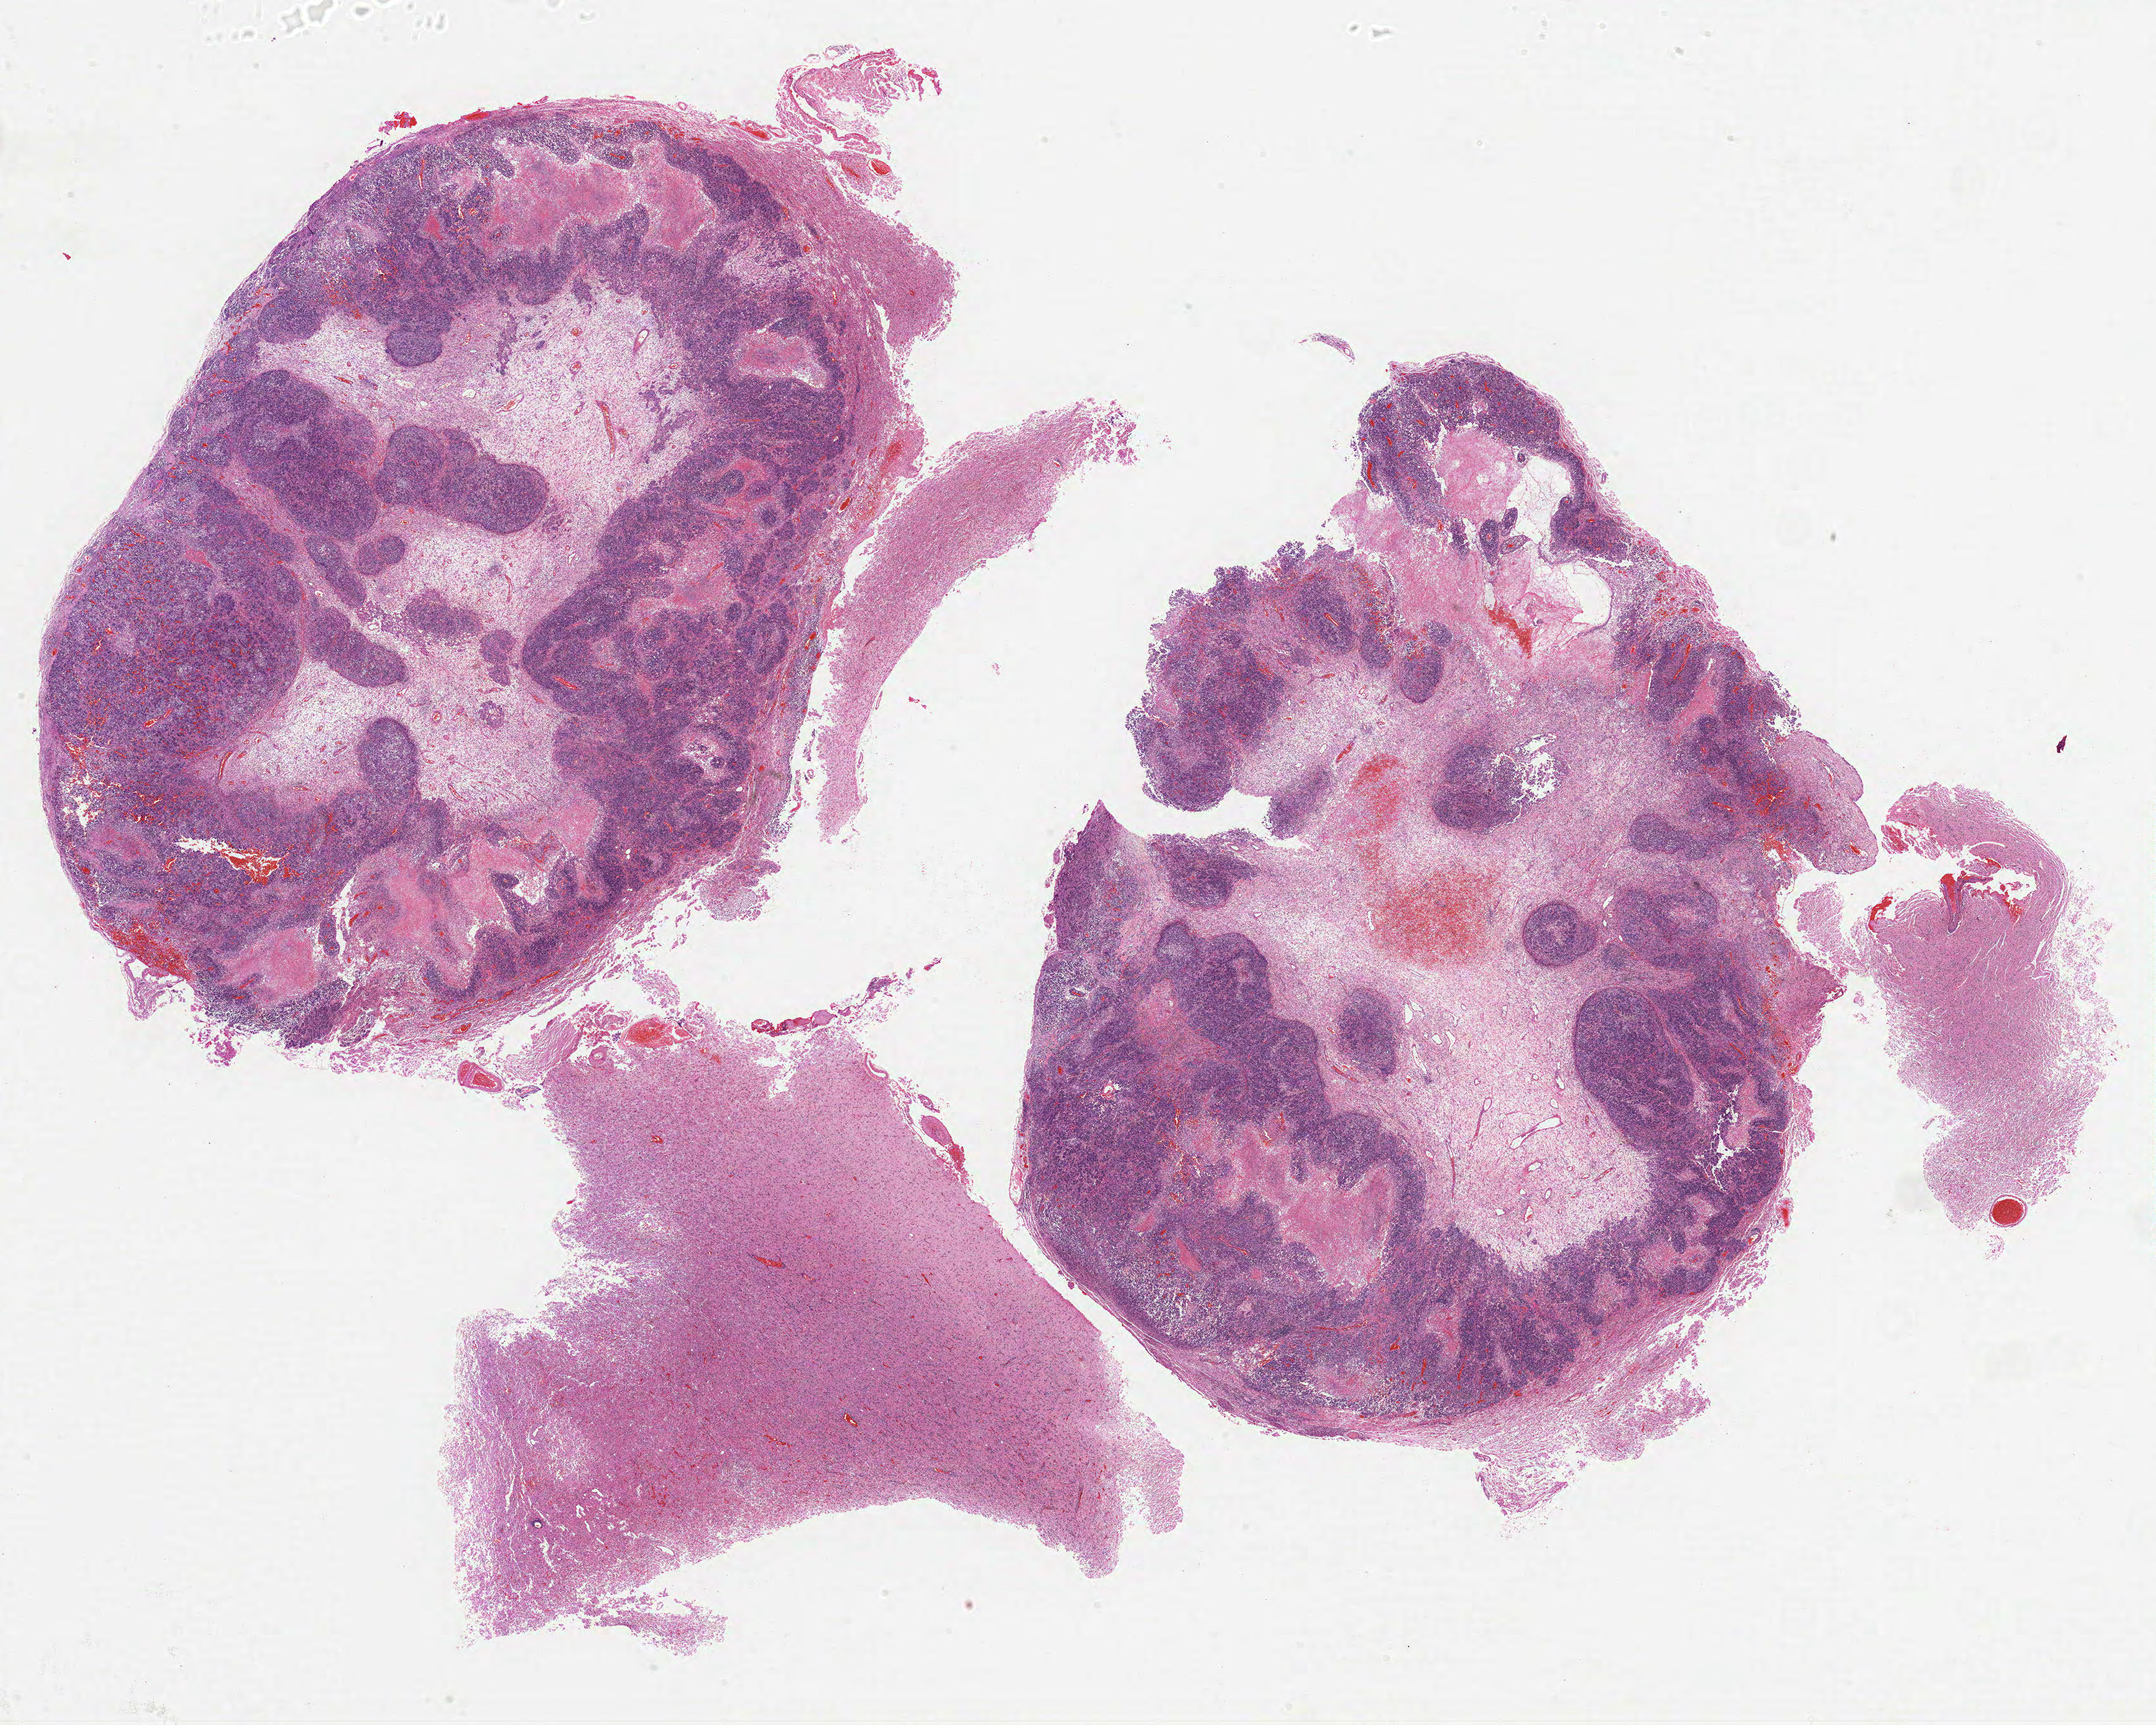
H&E-stained whole-slide image, shown as a low-resolution overview of the whole scanned area (about 27.0 x 21.6 mm), formalin-fixed paraffin-embedded (FFPE) diagnostic section, primary tumour sample from the brain. Patient: male, age at initial diagnosis 64 years.
* histologic diagnosis: Glioblastoma